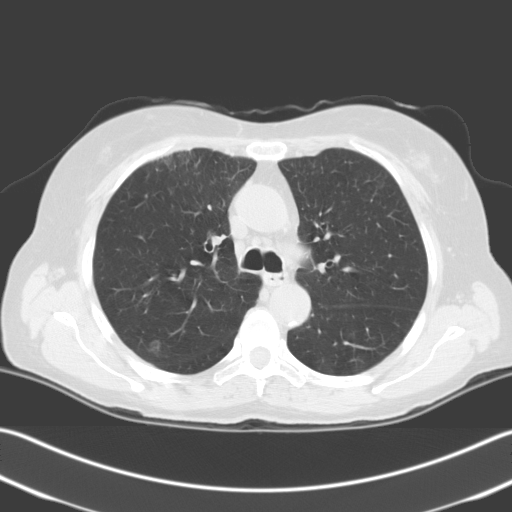
Axial slice from a low-dose chest CT screening exam. First (baseline) screen. Lung window (W 1500 / L -600 HU). 3.2 mm slice thickness. Standard (soft-tissue) reconstruction kernel (C). 512 × 512 image matrix, field of view 348 × 348 mm. Female participant, aged 67 years at enrolment. Current smoker at enrolment.
Expert-annotated lung lesion, box from (x=122, y=326) to (x=180, y=375) px. The screening reader recorded 2 non-calcified nodules or masses ≥4 mm on this exam (right upper lobe, right upper lobe); which of them this box marks is not recorded. Lung cancer was diagnosed 24 days after this screen: squamous cell carcinoma, NOS, right upper lobe, stage IIIA (AJCC 6th edition), 56 mm at pathology.